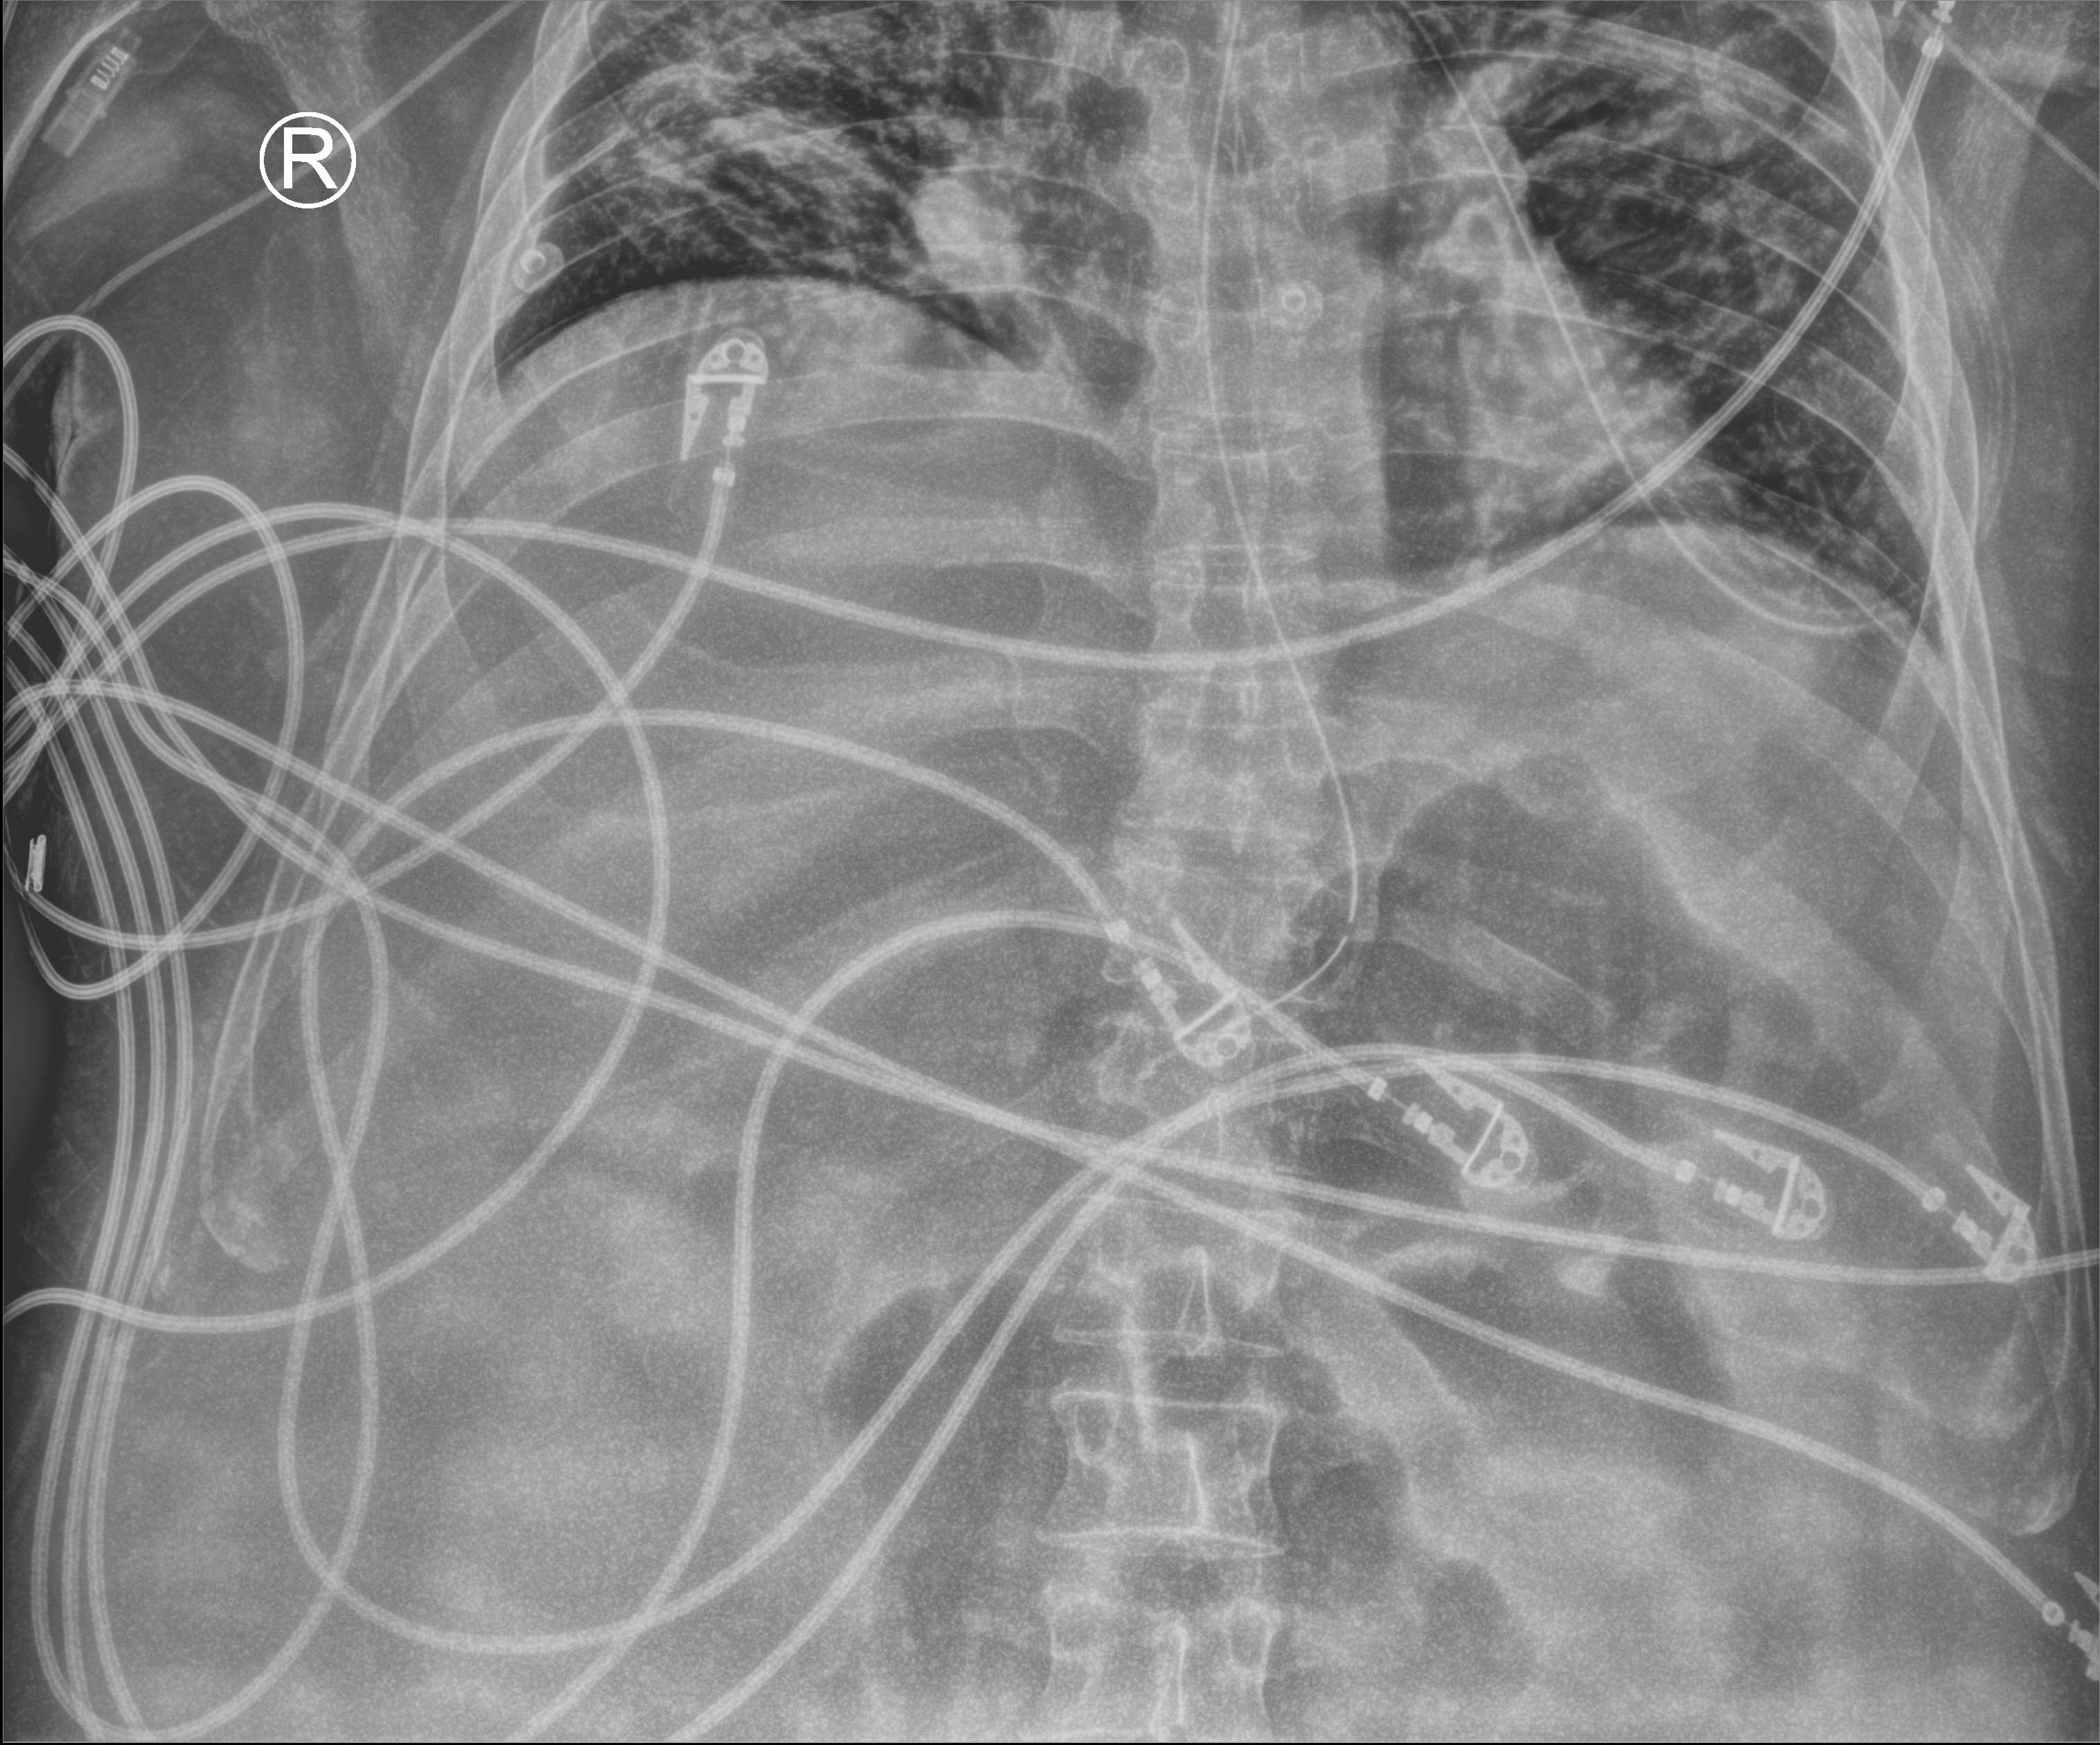
Portable abdomen radiograph, anteroposterior (AP) projection. Adult patient hospitalised with COVID-19, age 18–59 years.
Admission-level facts for this patient (not findings on this image; timing relative to this image not recorded):
- mechanically ventilated during this hospital stay: yes
- chronic kidney disease (admission record): no
- admitted to intensive care during this hospital stay: yes